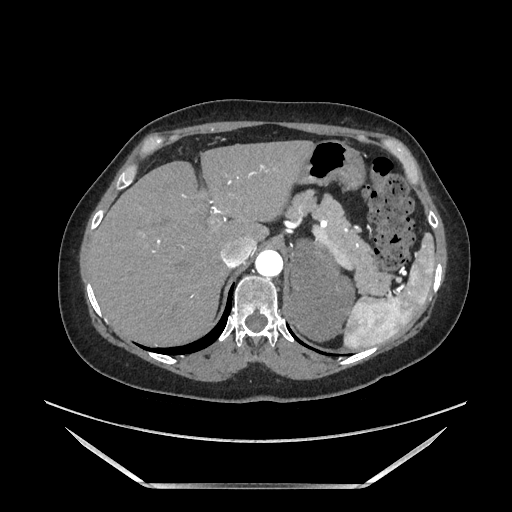
Contrast-enhanced abdominal CT, one axial slice; position 136 of 205 along the scan axis; soft-tissue window (W 400 / L 40 HU); 1.25 mm slice thickness; 512 × 512 image matrix, field of view 440 × 440 mm. Female patient. From the clinical record (not read from this slice): diagnosis: adrenocortical carcinoma; tumour side: left adrenal; tumour size at pathology: 12.5 cm.
Annotated regions visible in this slice (semi-automatically segmented with operator editing):
- mass: bounding box <293,243,353,340> (left, top, right, bottom; pixels)